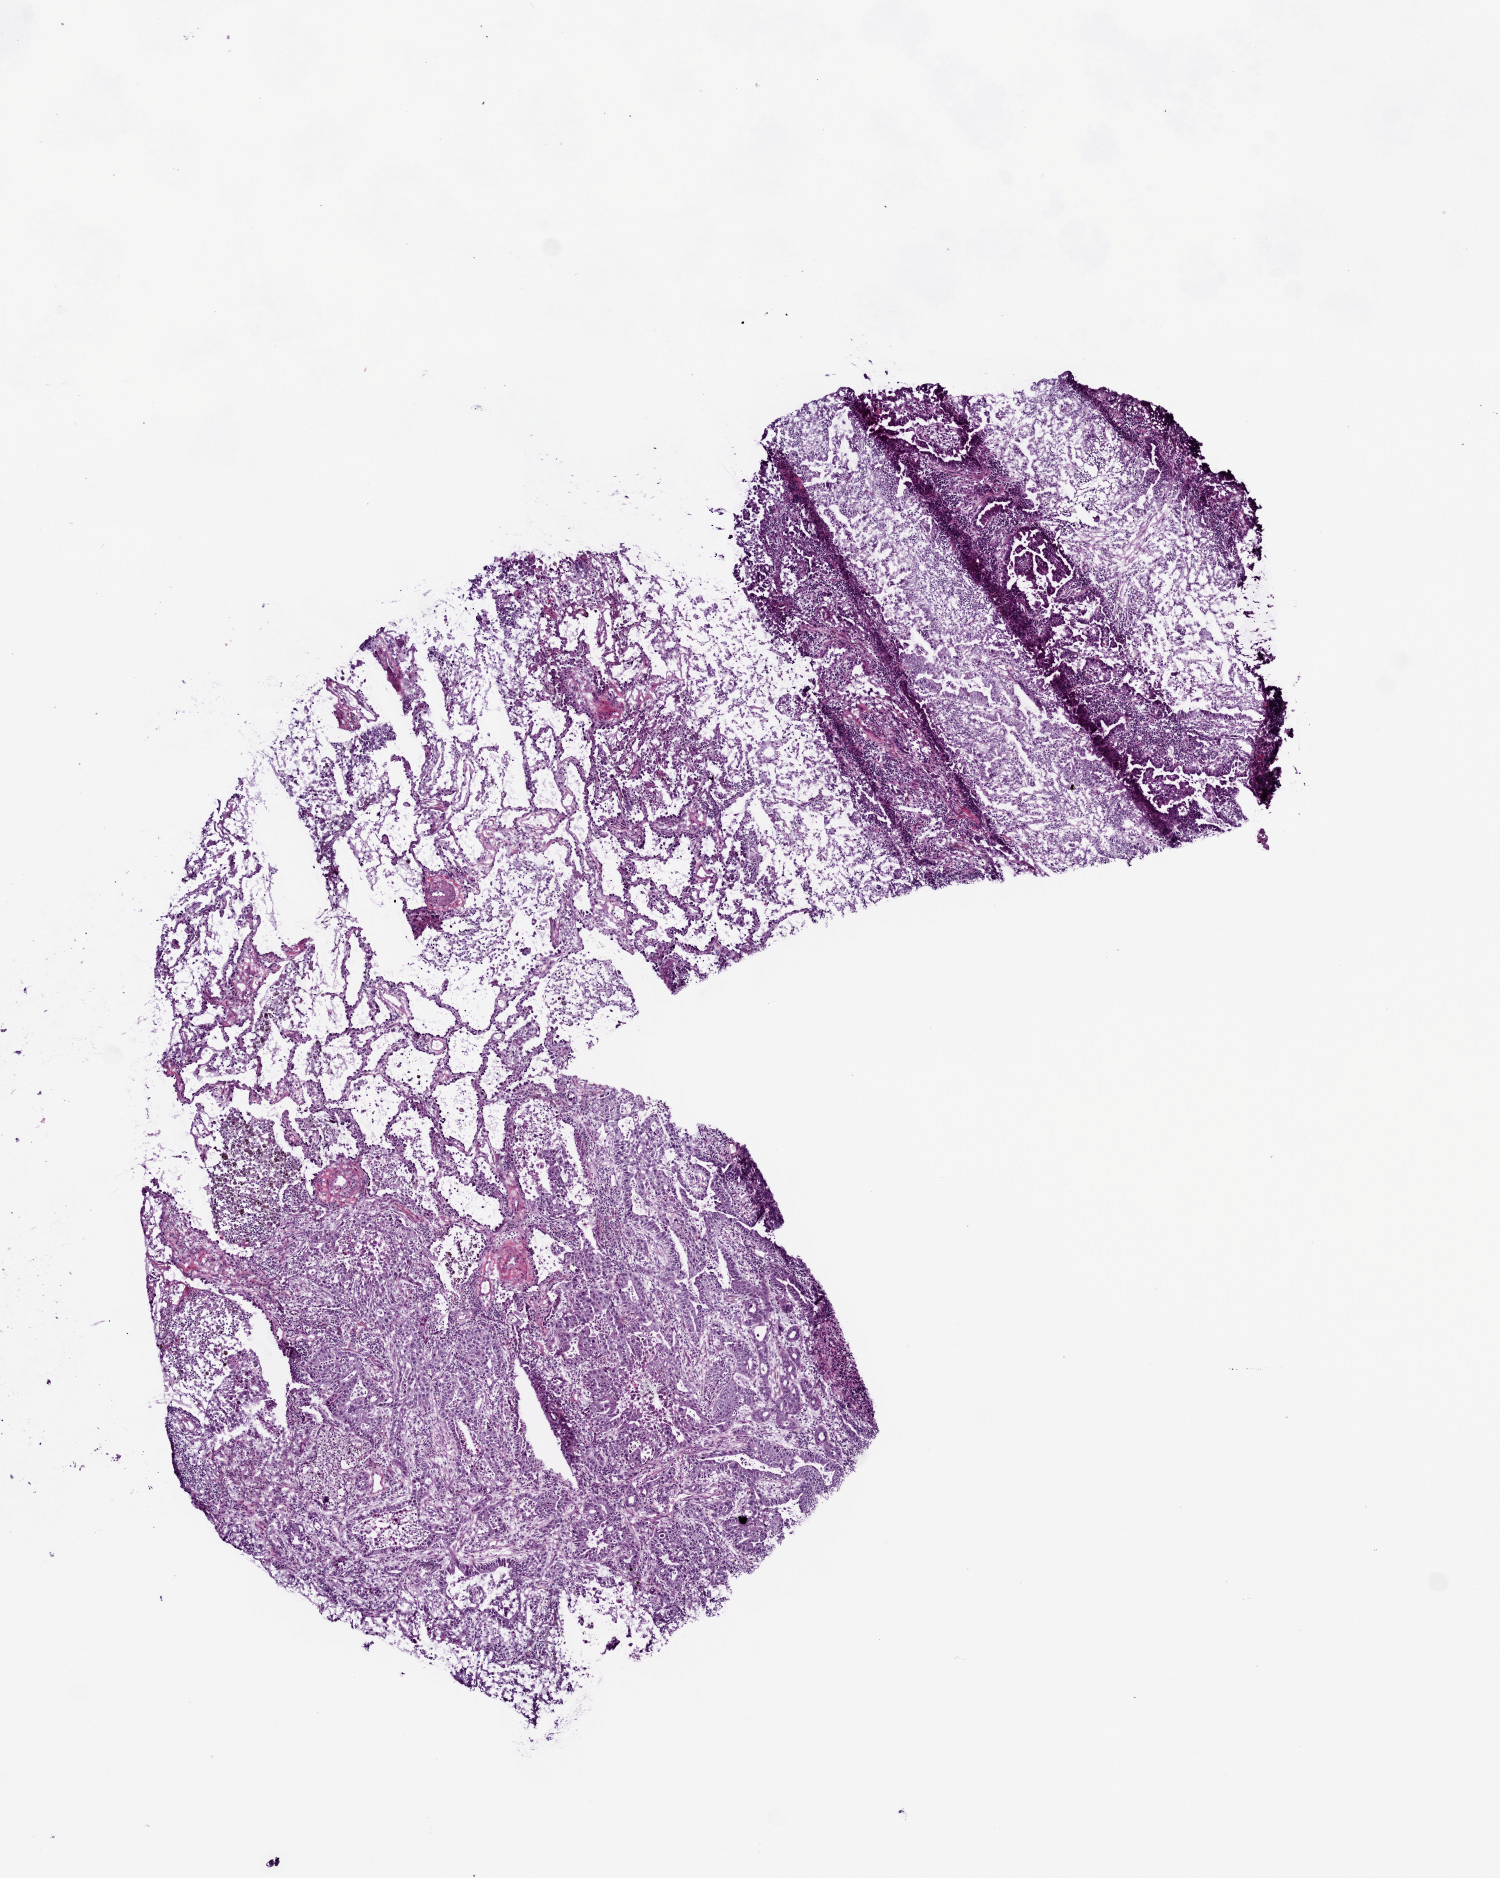
H&E-stained whole-slide image, low-resolution overview of the scanned area, about 6.0 x 7.5 mm, frozen section, primary tumour sample from the lung. Patient: male, age at initial diagnosis 68 years. Composition of this section per pathologist review: tumour cells 75%, tumour nuclei 60%, normal cells 20%, stromal cells 0%, necrosis 5%. Inflammatory infiltration, as recorded: lymphocyte infiltration 20%, monocyte infiltration 2%, neutrophil infiltration 20%.
TNM: T2b N1 M0. Diagnosis: Adenocarcinoma with mixed subtypes. AJCC pathologic stage: IIB. Laterality: right.